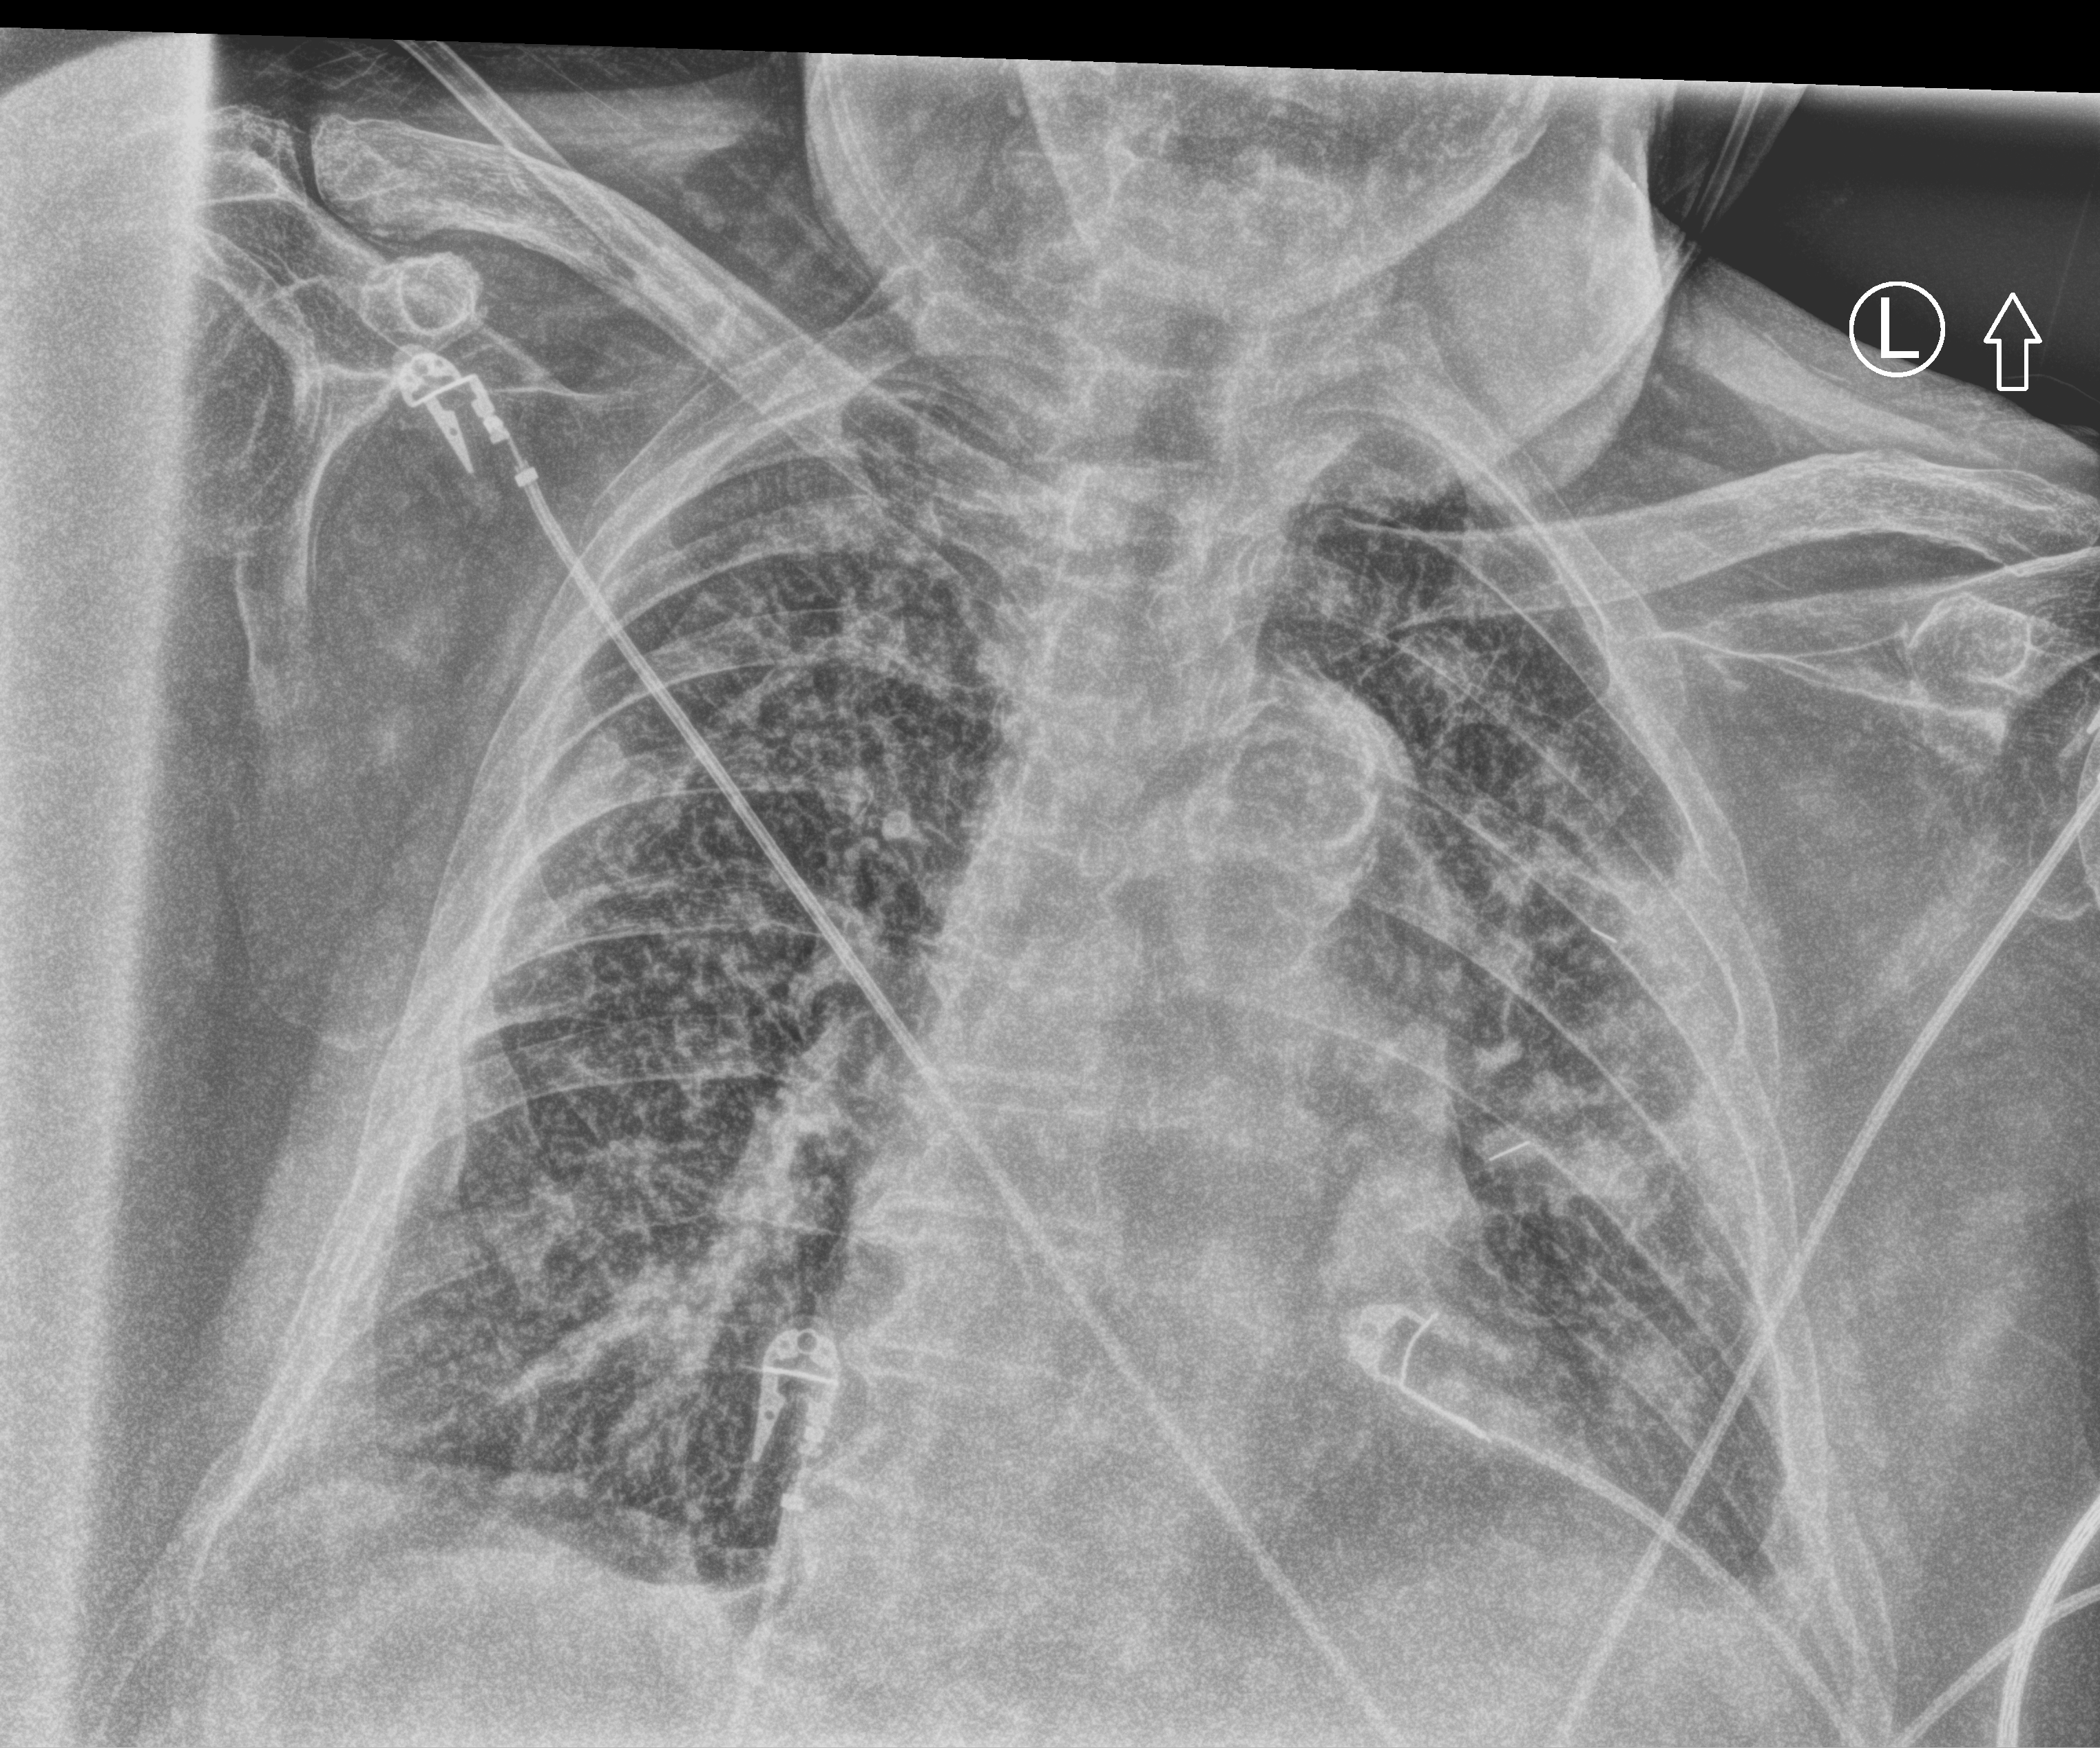
Portable chest radiograph. Male patient hospitalised with COVID-19, age 75–90 years.
Hospital-stay facts (about this admission, not read from this image; timing relative to this image not recorded): admitted to intensive care during this hospital stay: no; mechanically ventilated during this hospital stay: no.